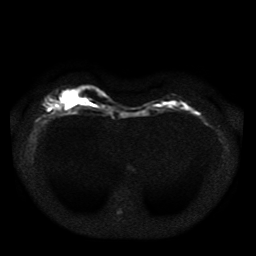
Breast MRI, one axial slice; position 11 of 41 along the scan axis; diffusion-weighted series; image 2 of 4 stored at this slice position (different b-values; order by instance number); 1.5 T; 5 mm slice thickness; 256 × 256 image matrix, field of view 330 × 330 mm. Female patient.
Structures marked on this image (expert manual segmentation):
- tumour on diffusion-weighted imaging: bounding box <47,103,61,111> (left, top, right, bottom; pixels)